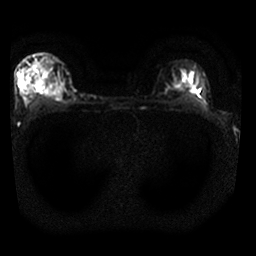
Breast MRI, one axial slice; slice 21 of 25 in the series (ordered by position); diffusion-weighted series; image 2 of 4 stored at this slice position (different b-values; order by instance number); 1.5 T; 4 mm slice thickness; 256 × 256 image matrix, field of view 310 × 310 mm. Female patient.
Outlined on this slice (outlined manually by an expert reader):
- tumour on diffusion-weighted imaging: bounding box (x1, y1, x2, y2) in pixels: (37, 78, 62, 98)